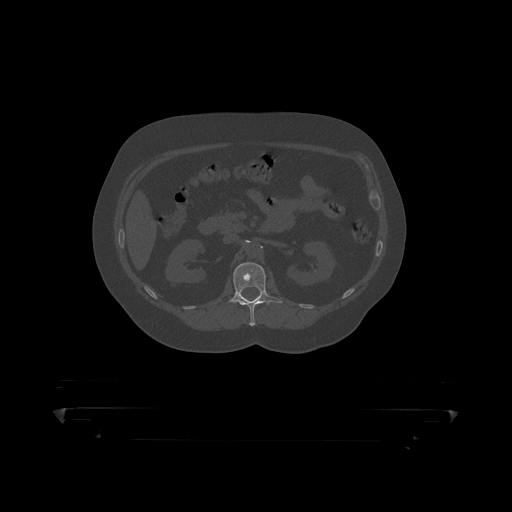
CT including the spine, one axial slice; reconstruction kernel STANDARD; bone window (W 1800 / L 400 HU); 1.25 mm slice thickness; 512 × 512 image matrix. Patient: male, 60 years. From the clinical record (not read from this slice): primary cancer: prostate.
Structures marked on this image (semi-automatically segmented with operator editing):
- L1 vertebra: bounding box (x1, y1, x2, y2) in pixels: (228, 263, 283, 319)